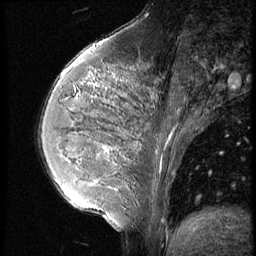
Breast MRI (dynamic contrast-enhanced), one sagittal slice. Position 21 of 56 along the scan axis. 3 images stored at this slice position (order not interpretable as contrast timing). 1.5 T. TE 4.2 ms, TR 9 ms. 256 × 256 image matrix, field of view 180 × 180 mm. Patient: female, 35 years. Case-level facts recorded for this patient, not image findings: setting: breast cancer imaged before/during neoadjuvant chemotherapy; receptor status: HR-positive, HER2-negative.
Outlined on this slice (semi-automatically segmented with operator editing):
- analysis volume of interest (the breast-tissue region the enhancement analysis was run in; not a lesion): bounding box <63,60,190,218> (left, top, right, bottom; pixels)
- tumour enhancement mask (voxels above the 140 % enhancement threshold inside the analysis volume of interest): <63,69,170,186>